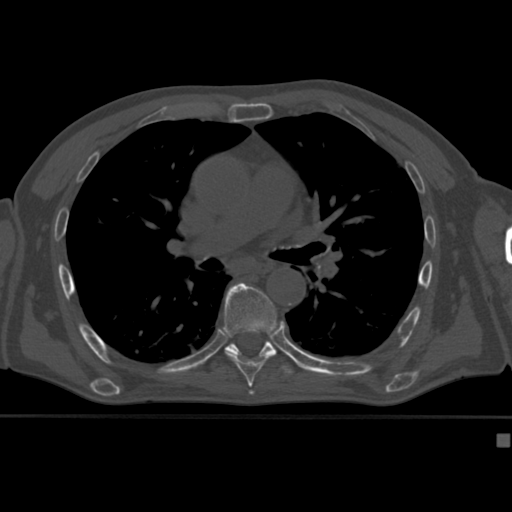
CT including the spine, one axial slice. Slice 274 of 430 in the series (ordered by position). 120 kVp. Bone window (W 1800 / L 400 HU). 1.5 mm slice thickness. 512 × 512 image matrix, field of view 337 × 337 mm. Patient: male, 64 years. From the clinical record (not read from this slice): primary cancer: uterus.
Outlined on this slice (semi-automatically segmented with operator editing):
- T7 vertebra: bounding box <223,282,277,382> (left, top, right, bottom; pixels)
- T8 vertebra: <224,340,293,374>